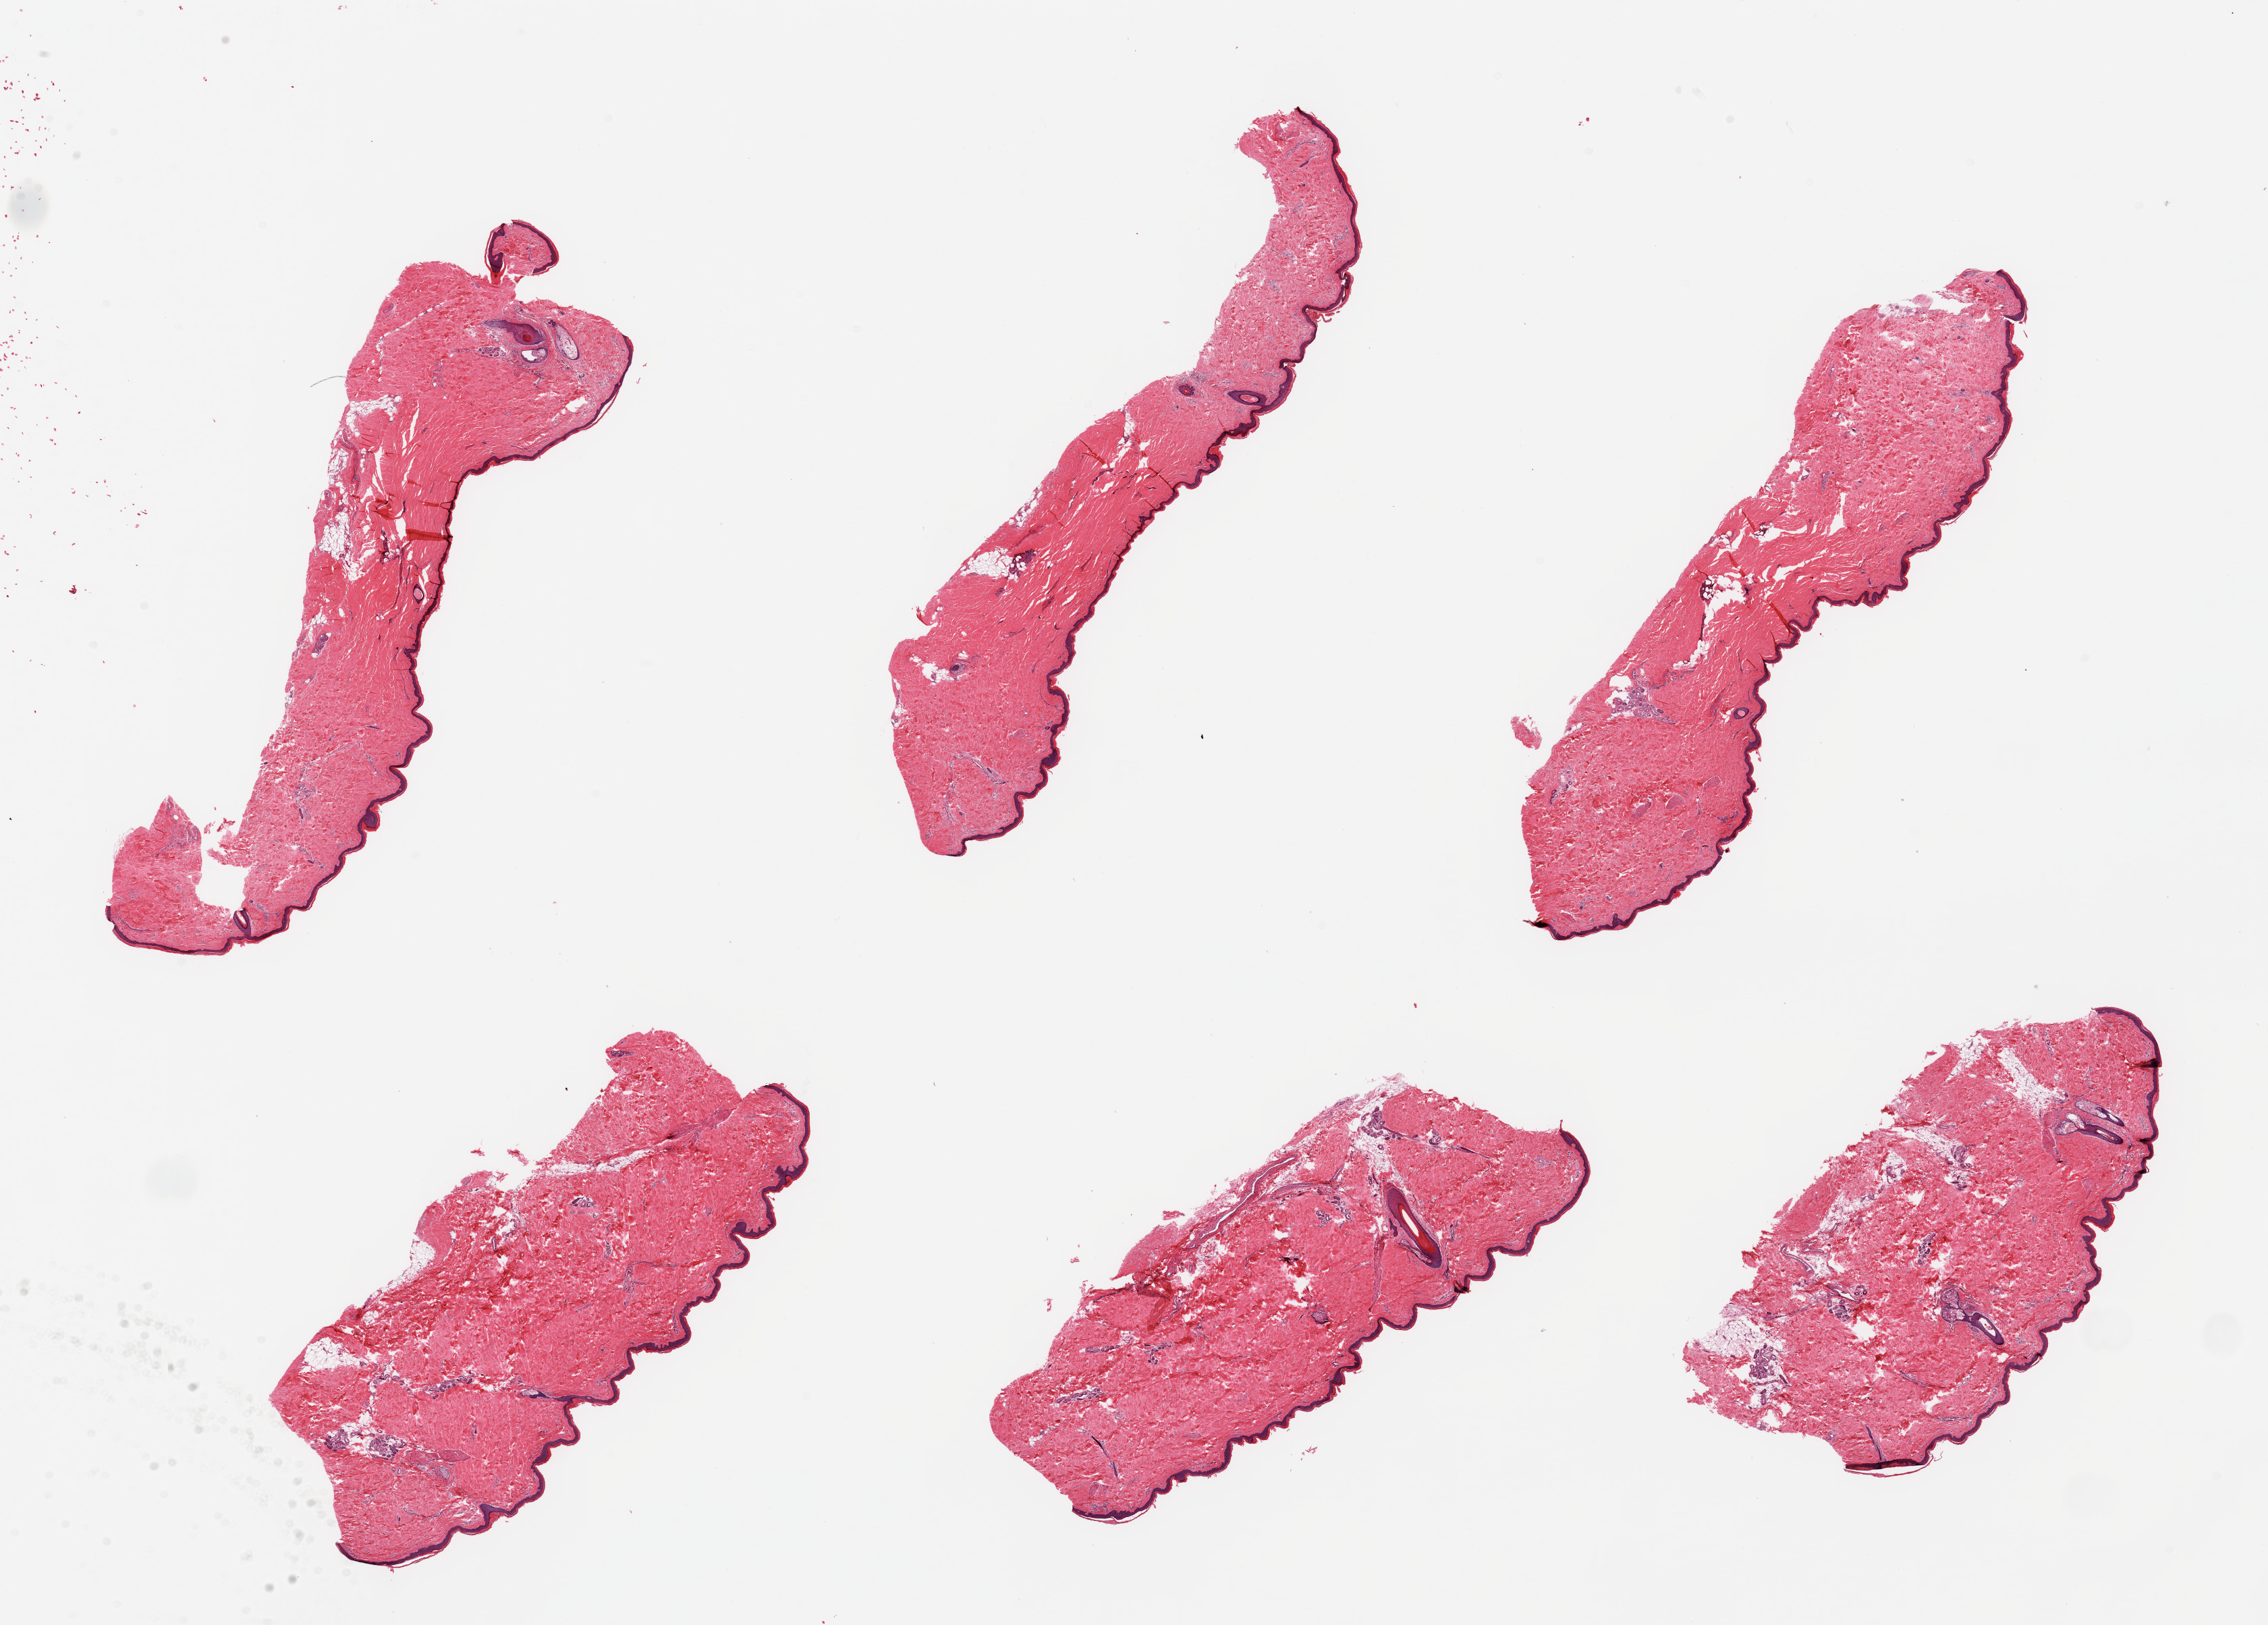
Whole-slide image, H&E stain, whole scanned area (about 26.6 x 19.0 mm, from a 20x scan) shown as a low-resolution overview. PAXgene-fixed, paraffin-embedded tissue. Sampled site (target tissue): skin of lower leg. Donor tissue sample. Donor sex: male.
Review note (as recorded): 6 pieces; well trimmed, minimal internal fat, epidermis measures 35 microns.